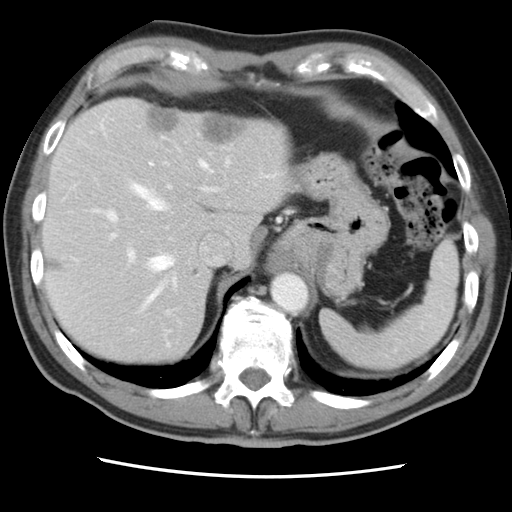
Contrast-enhanced abdominal CT, one axial slice. Position 64 of 83 along the scan axis. 120 kVp. Intravenous contrast given. Soft-tissue window (W 400 / L 40 HU). 5 mm slice thickness. 512 × 512 image matrix. Male patient, age 69 years. From the clinical record (not read from this slice): diagnosis: colorectal cancer liver metastases, imaged before liver resection; multiple liver metastases: yes; largest metastasis: 3.5 cm; disease in both lobes: no.
Structures marked on this image (expert manual segmentation):
- hepatic veins: bounding box (x1, y1, x2, y2) in pixels: (100, 118, 213, 303)
- liver: (44, 99, 287, 364)
- planned liver remnant (the part of the liver to remain after resection): (44, 145, 211, 363)
- portal vein (with intrahepatic branches): (104, 161, 210, 263)
- liver metastasis: (148, 112, 179, 132)
- liver metastasis: (191, 269, 200, 277)
- liver metastasis: (203, 121, 244, 143)